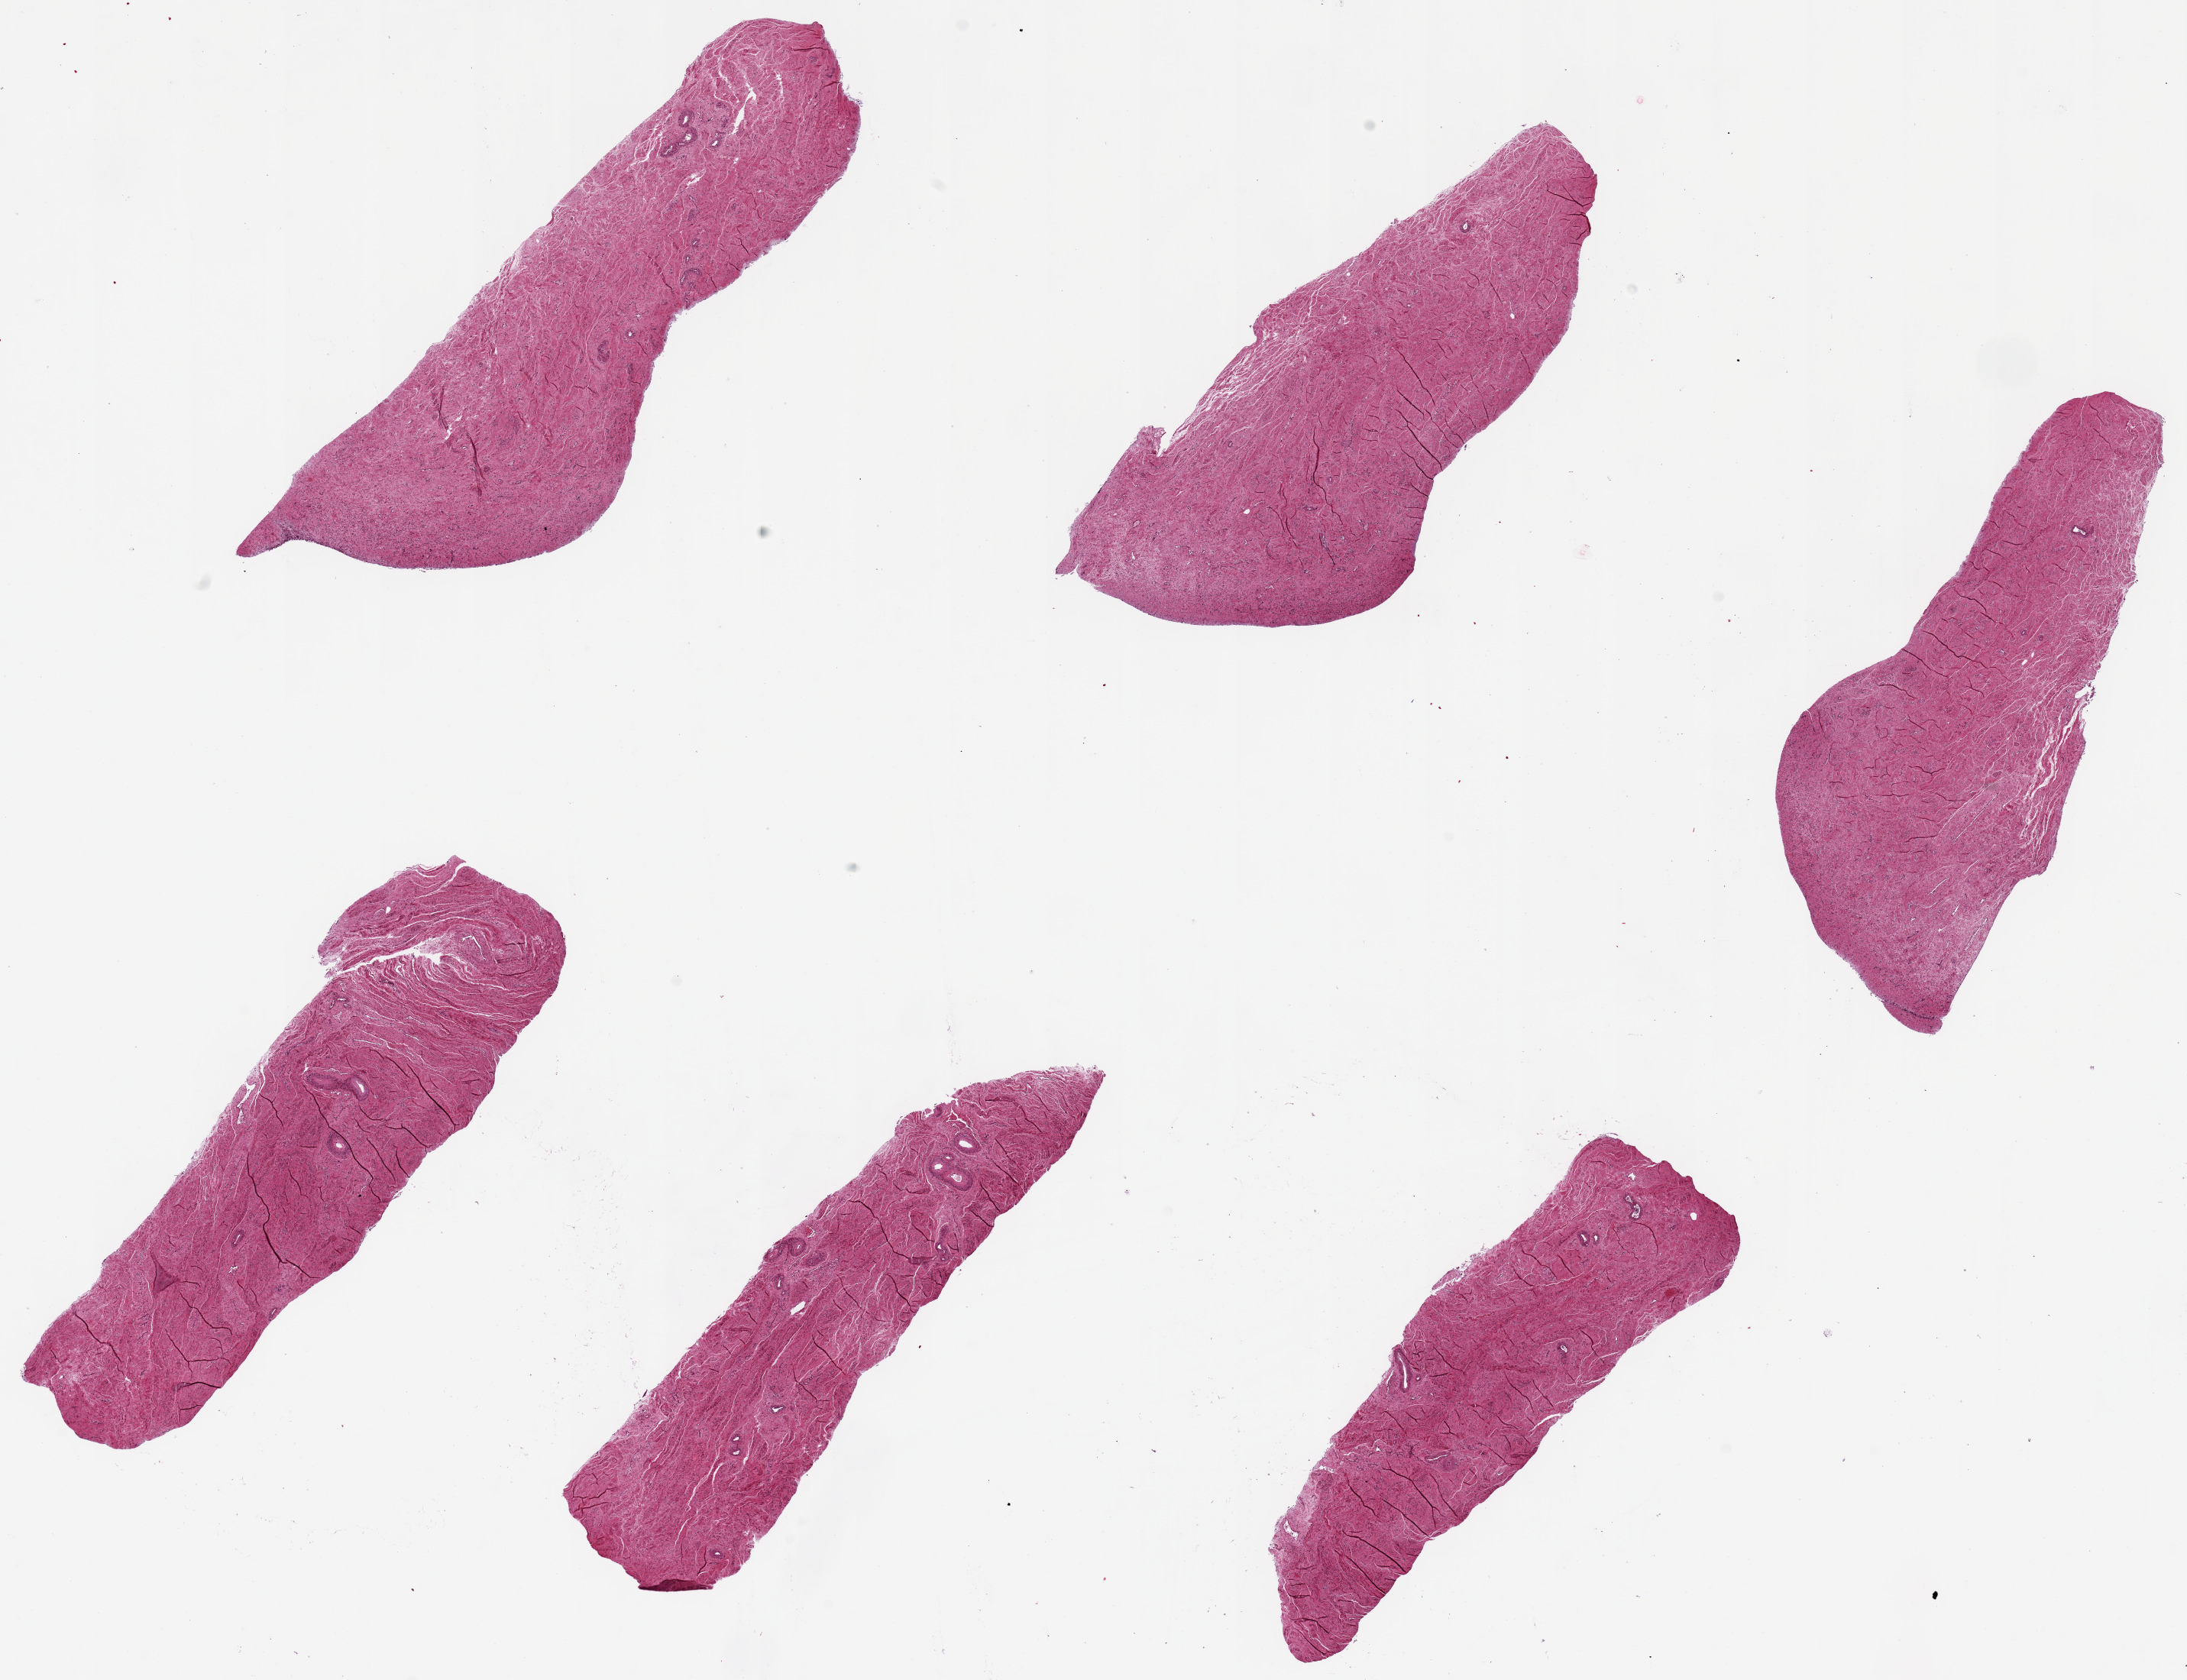
H&E whole-slide image, brightfield — a low-resolution overview of the entire scanned area, about 22.6 x 17.4 mm (acquisition: 20x scan); PAXgene-fixed paraffin-embedded (PFPE) section; sampled site (target tissue): vagina; donor tissue sample. Donor sex: female.
• pathologist's review note for this sample: 6 pieces, up to 8x2.5mm; mucosa completely sloughed/autolyzed